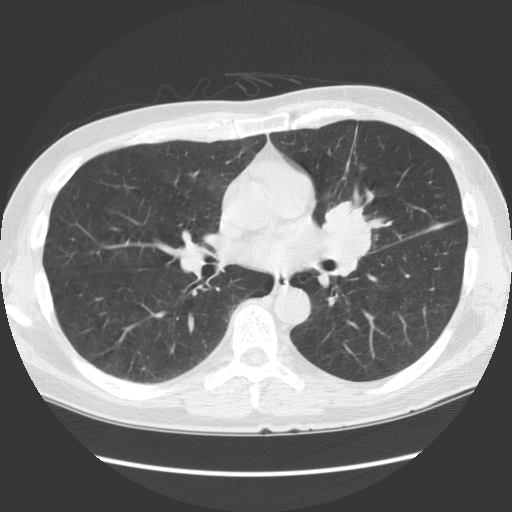
Low-dose screening chest CT, one axial slice. Slice 70 of 136 in the series (ordered by position). Reconstruction kernel STANDARD. Lung window (W 1500 / L -600 HU). 2.5 mm slice thickness. 512 × 512 image matrix, field of view 360 × 360 mm.
Outlined on this slice (outlined manually by an expert reader):
- lesion 1 (tumor, hilum of left lung): box from (x=322, y=201) to (x=372, y=257) px